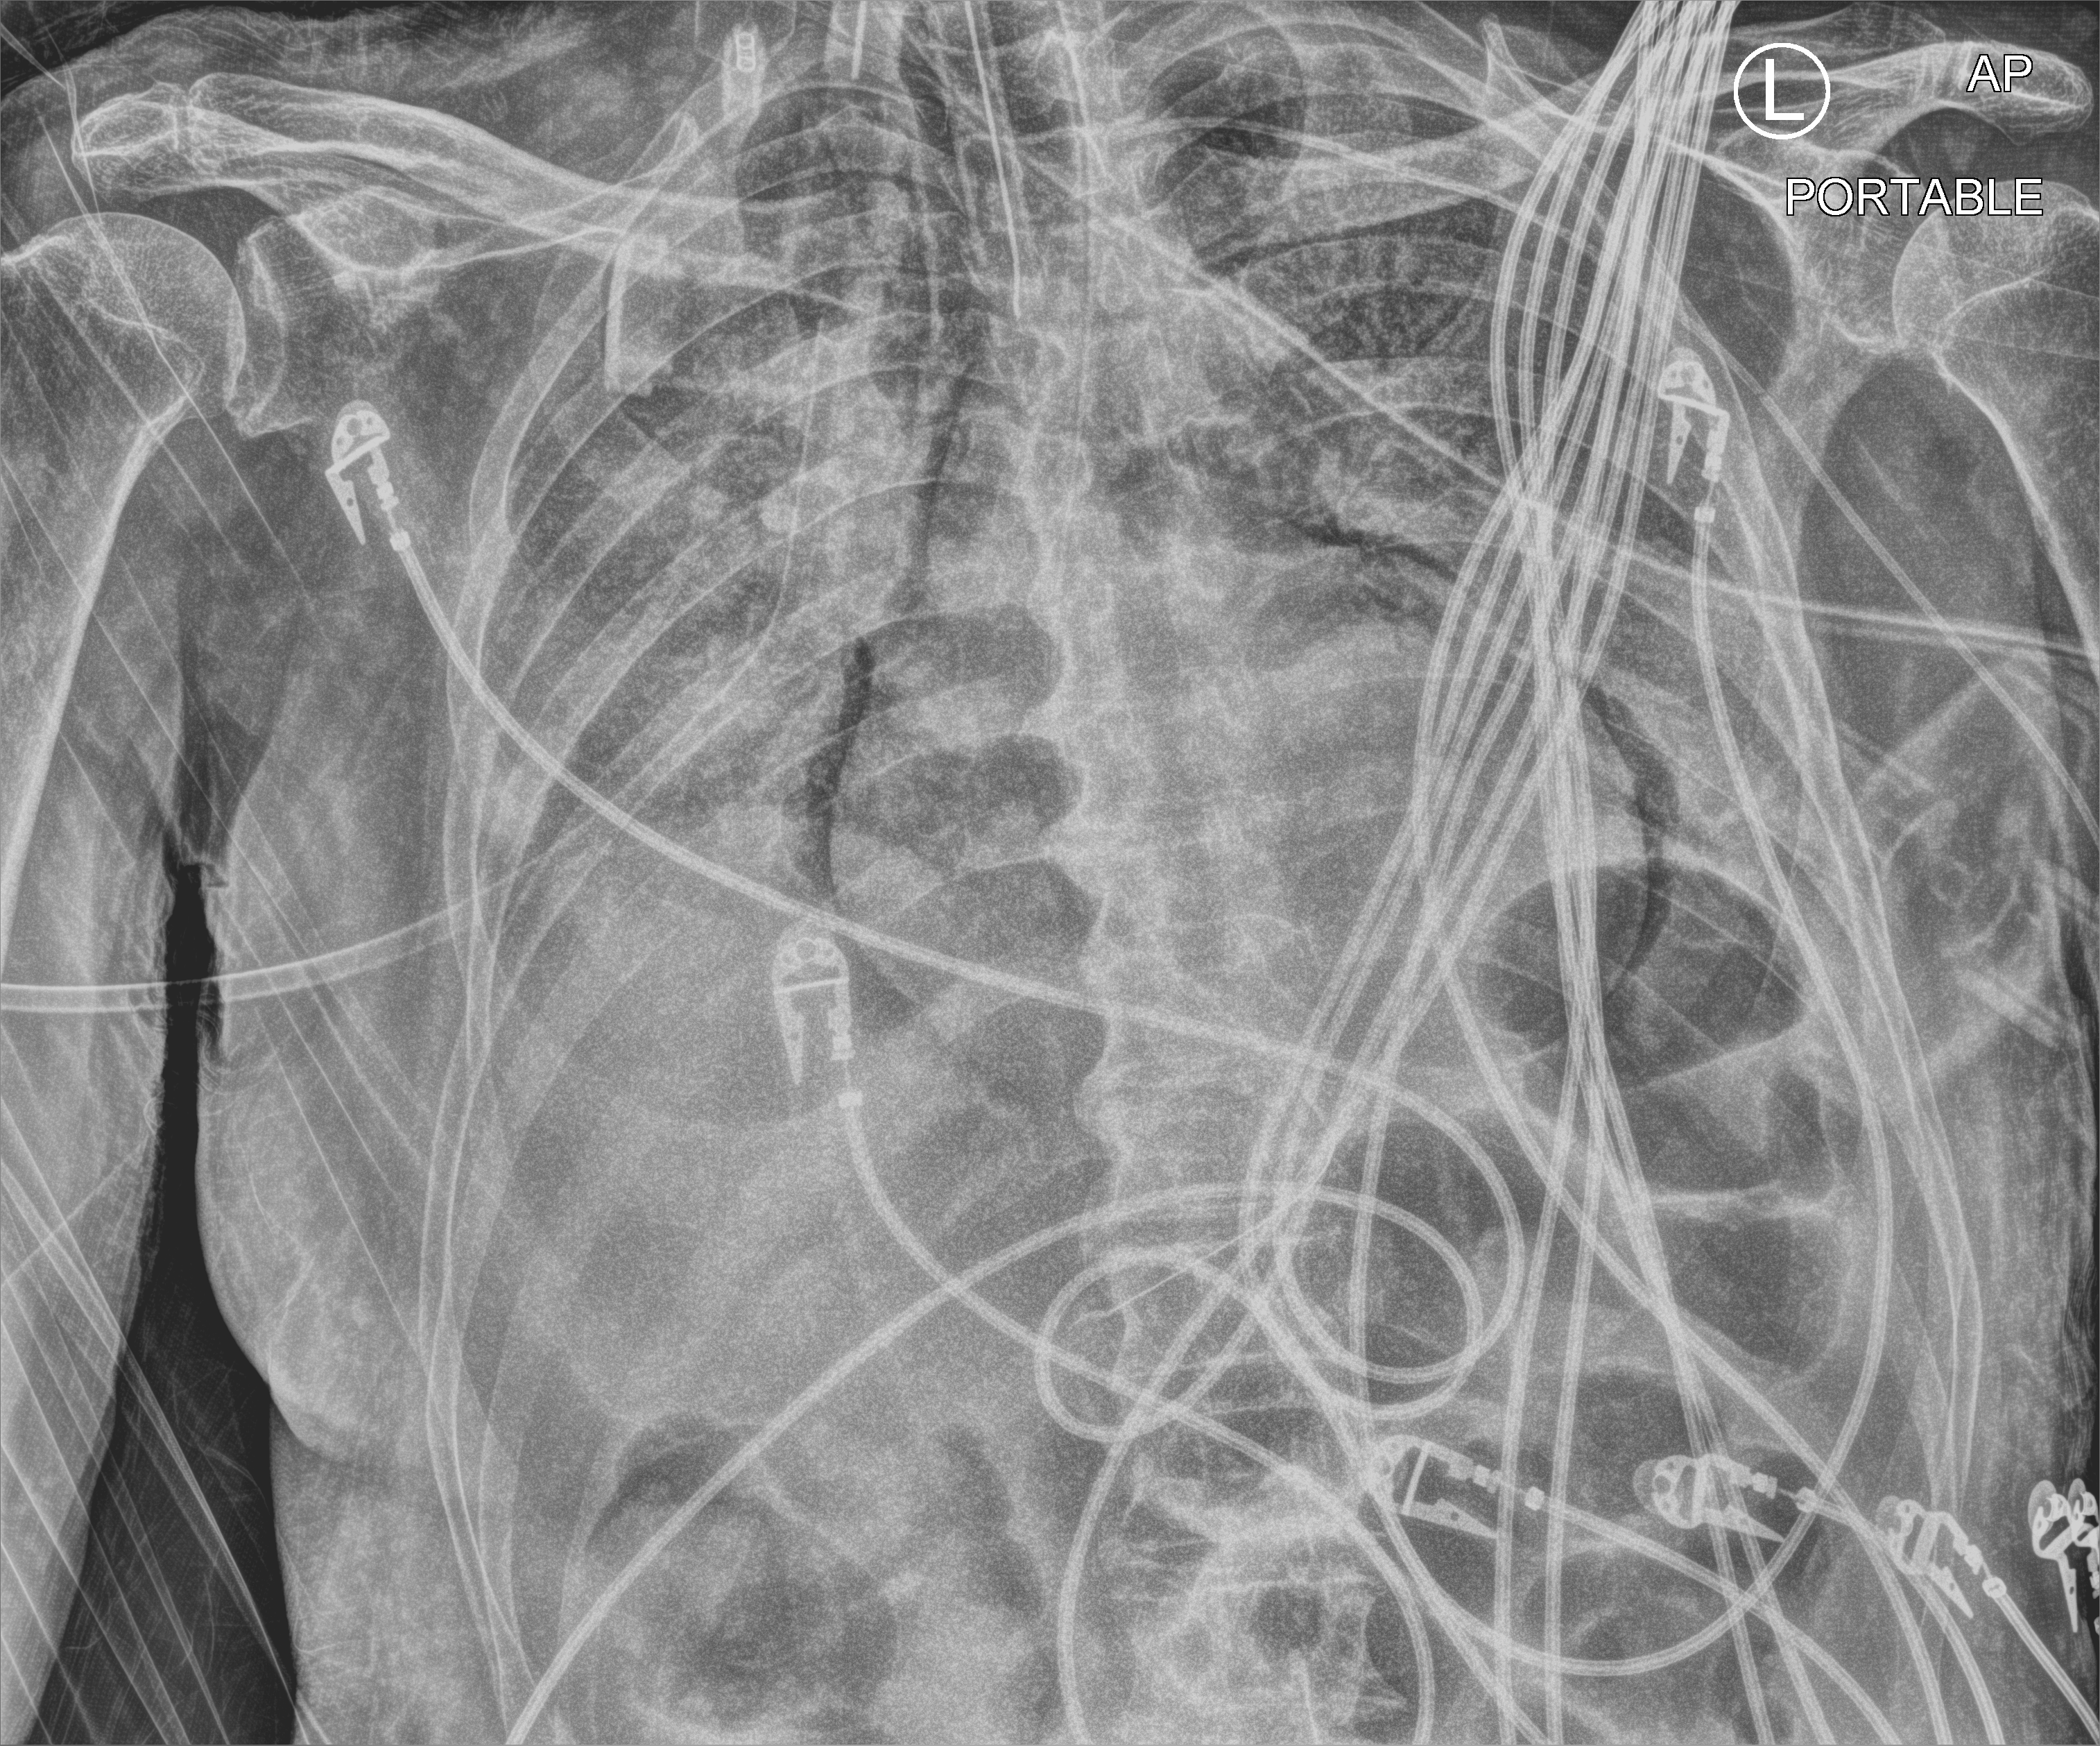
Bedside chest radiograph (computed radiography), anteroposterior (AP) projection. Patient hospitalised with COVID-19; male, aged 75–90 years.
From the hospital-stay record, not from the radiograph (when in the stay this image was taken is not recorded): length of hospital stay: 30 days; mechanically ventilated during this hospital stay: yes.